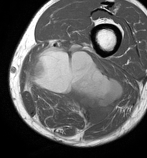
MRI of an extremity soft-tissue mass, one axial slice. Slice 34 of 86 in the series (ordered by position). MR volume resampled by the dataset authors to the PET/CT grid (not the native acquisition matrix). 3.27 mm slice thickness. 147 × 158 image matrix, field of view 144 × 154 mm. Male patient. From the clinical record (not read from this slice): histological type: undifferentiated pleomorphic liposarcoma; grade: high; site of the primary tumour: left thigh.
Annotated regions visible in this slice (expert contour drawn on MRI and transferred to this co-registered scan by the dataset authors):
- gross tumour volume including surrounding oedema: bounding box <25,40,122,127> (left, top, right, bottom; pixels)
- gross tumour volume (mass): <28,49,122,125>